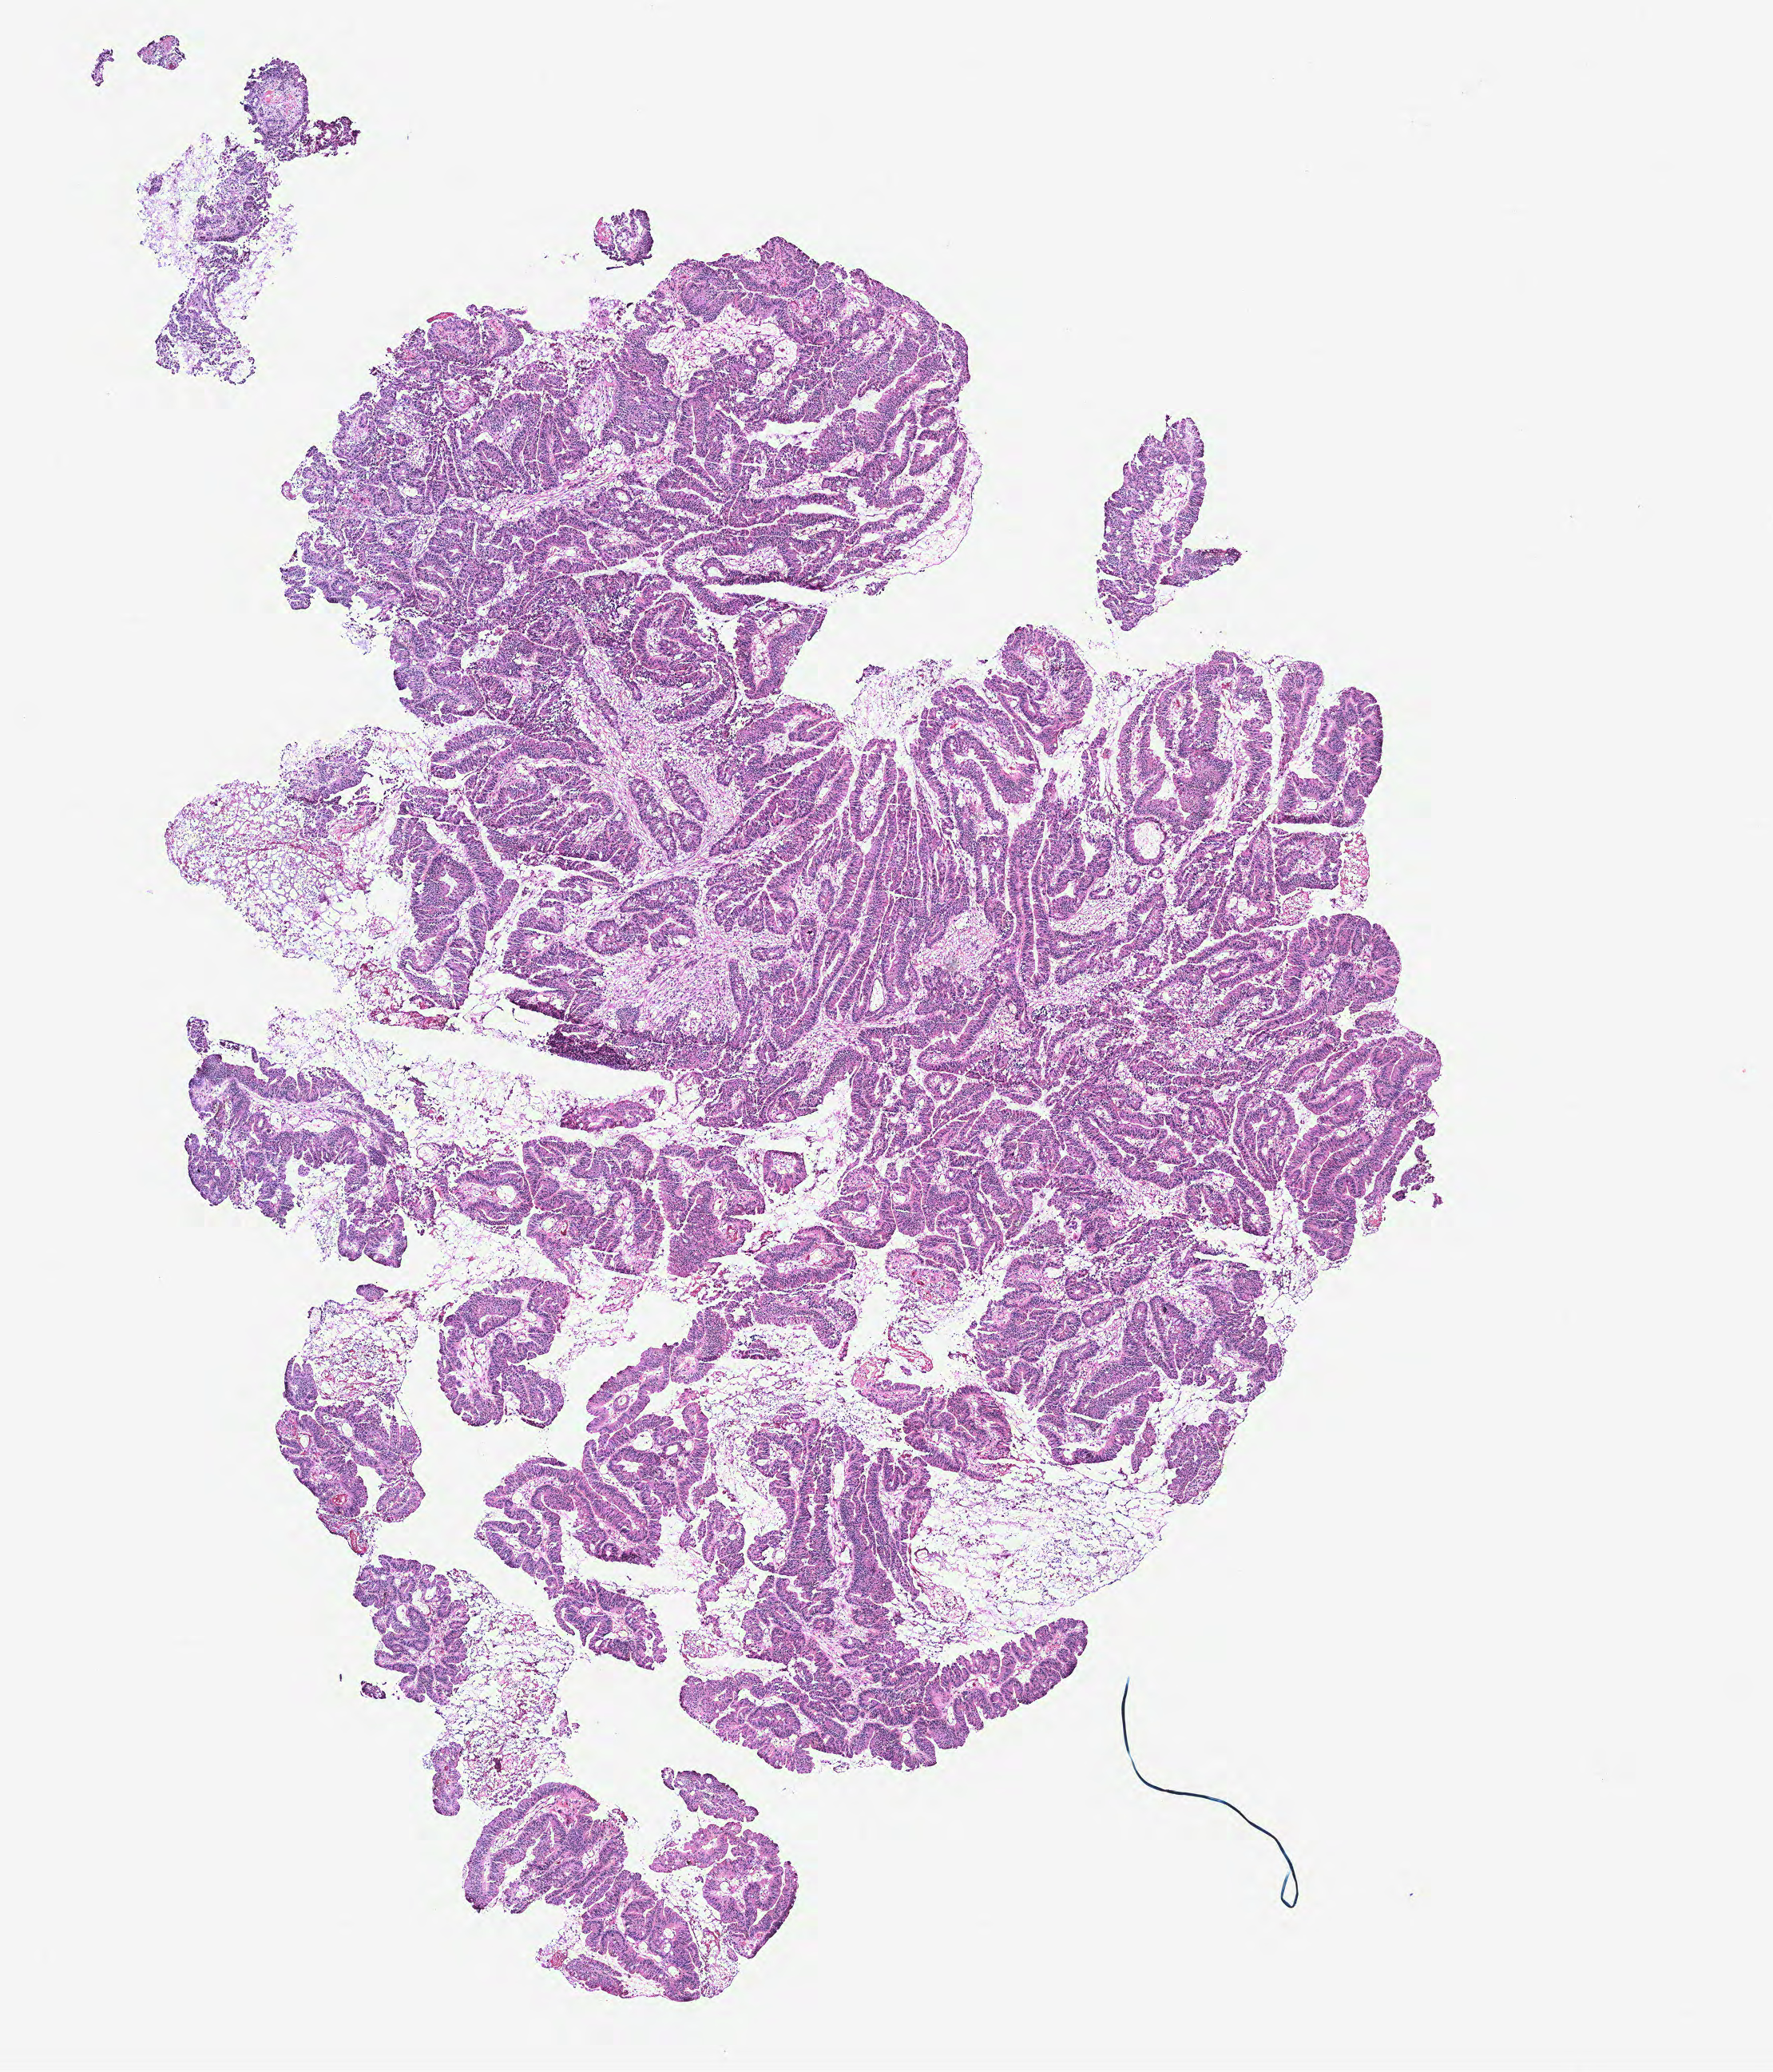
Whole-slide histology image, H&E — low-resolution overview of the scanned area, about 8.9 x 10.4 mm, colon, normal (non-tumour) tissue. Male, 51 y/o.
- this section: normal (non-tumour) tissue from the same patient
- patient diagnosis: Adenocarcinoma, NOS